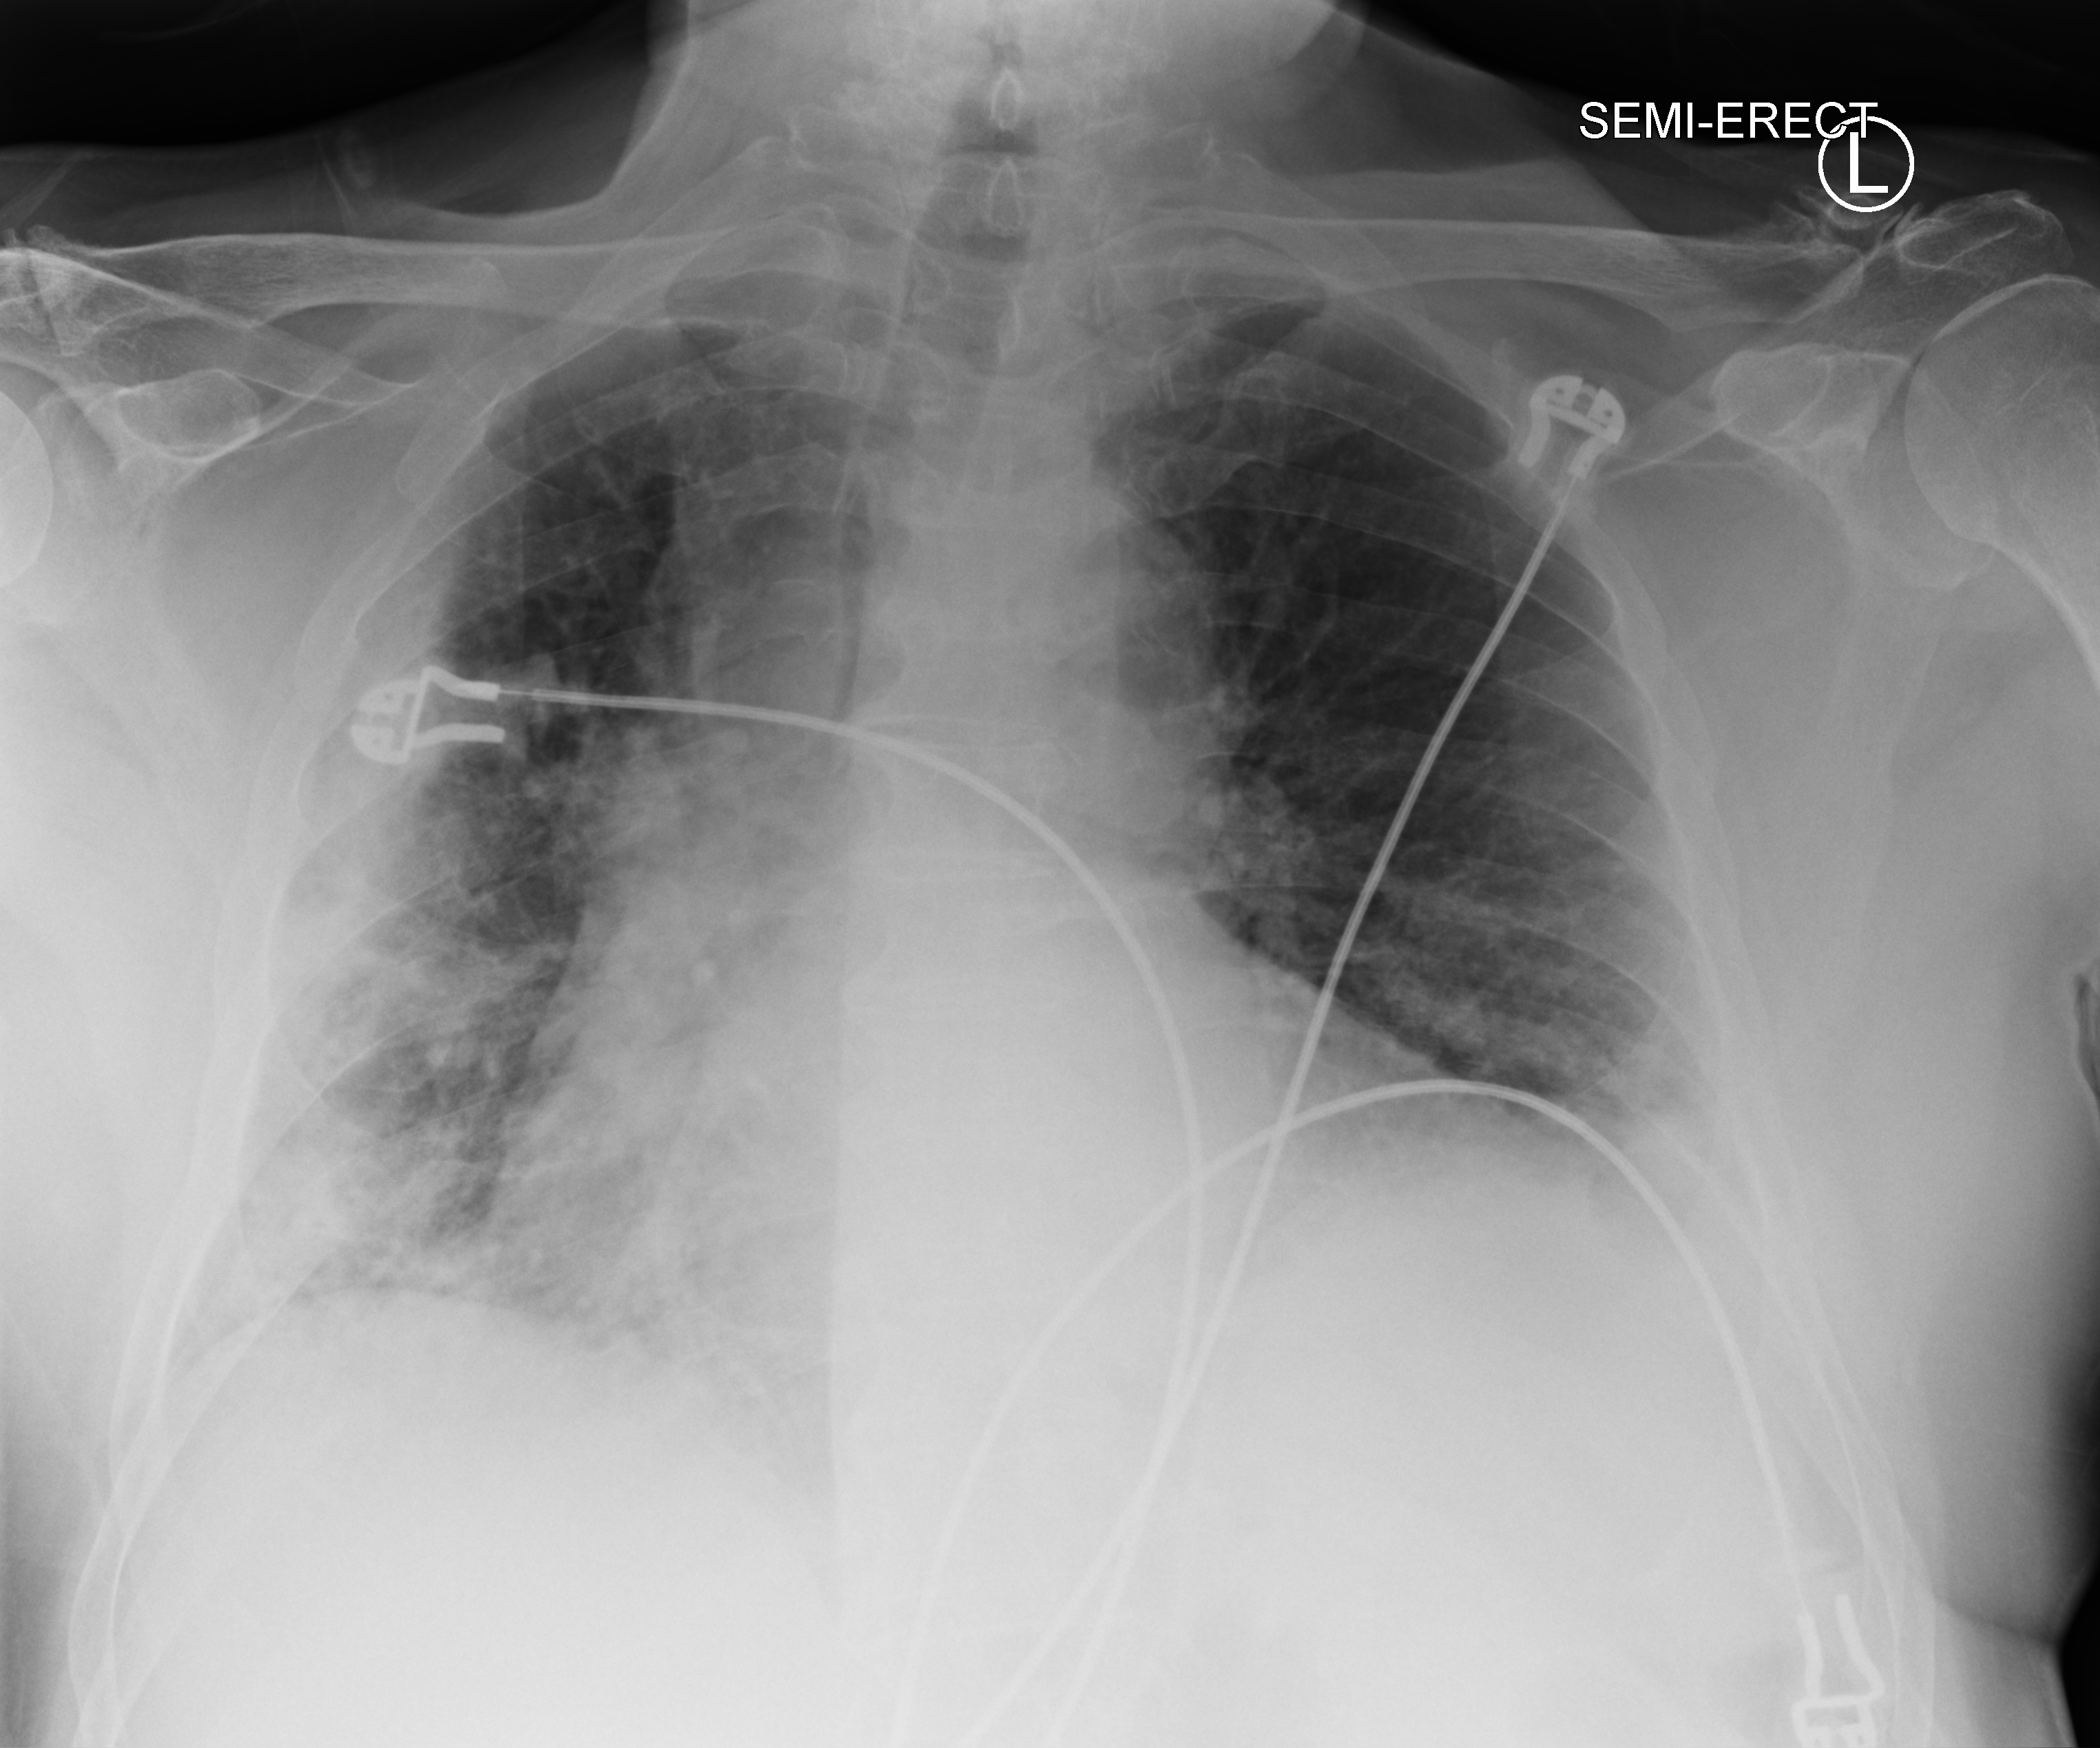
Chest X-ray (portable), anteroposterior (AP) projection. Male patient hospitalised with COVID-19, age 75–90 years.
Hospital-stay facts (about this admission, not read from this image; timing relative to this image not recorded):
- admitted to intensive care during this hospital stay: no
- diabetes (admission record): no
- length of hospital stay: 6 days